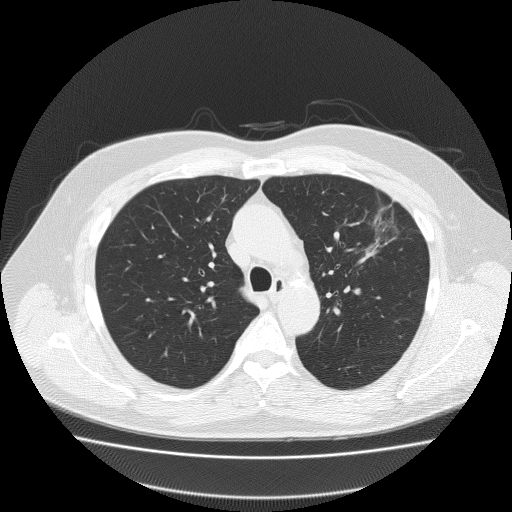
Low-dose screening chest CT, axial slice. First (baseline) screen. Lung window (W 1500 / L -600 HU). 2 mm slice thickness. 120 kVp. Male, age 62 years at enrolment. Former smoker at enrolment.
Expert-annotated lung lesion, box from (x=359, y=194) to (x=427, y=258) px. The exam's reader record, not a measurement of the box and not confirmed to be the same lesion: non-calcified nodule or mass ≥4 mm, left upper lobe, 18 × 8 mm, spiculated (stellate) margins, soft tissue attenuation. Participant outcome: lung cancer diagnosed 49 days after this screen — bronchiolo-alveolar adenocarcinoma, NOS, left upper lobe, well differentiated (G1), stage IA (AJCC 6th edition), 25 mm at pathology.